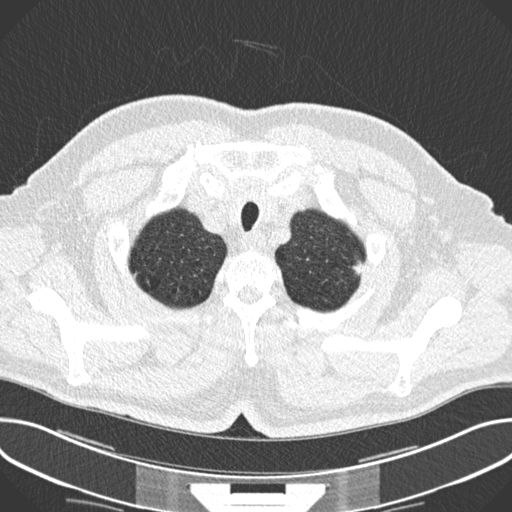
Low-dose screening chest CT, axial slice. First (baseline) screen. Lung window (W 1500 / L -600 HU). 2 mm slice thickness. 120 kVp. 512 × 512 image matrix. Male participant, aged 63 years at enrolment. Current smoker at enrolment.
Expert-annotated lung lesion, box from (x=343, y=250) to (x=387, y=284) px. The screening reader recorded 2 non-calcified nodules or masses ≥4 mm on this exam (left upper lobe, left upper lobe); which of them this box marks is not recorded. Participant outcome: lung cancer diagnosed 174 days after this screen — adenocarcinoma, NOS, left upper lobe, poorly differentiated (G3), stage IIIA (AJCC 6th edition), 11 mm at pathology.